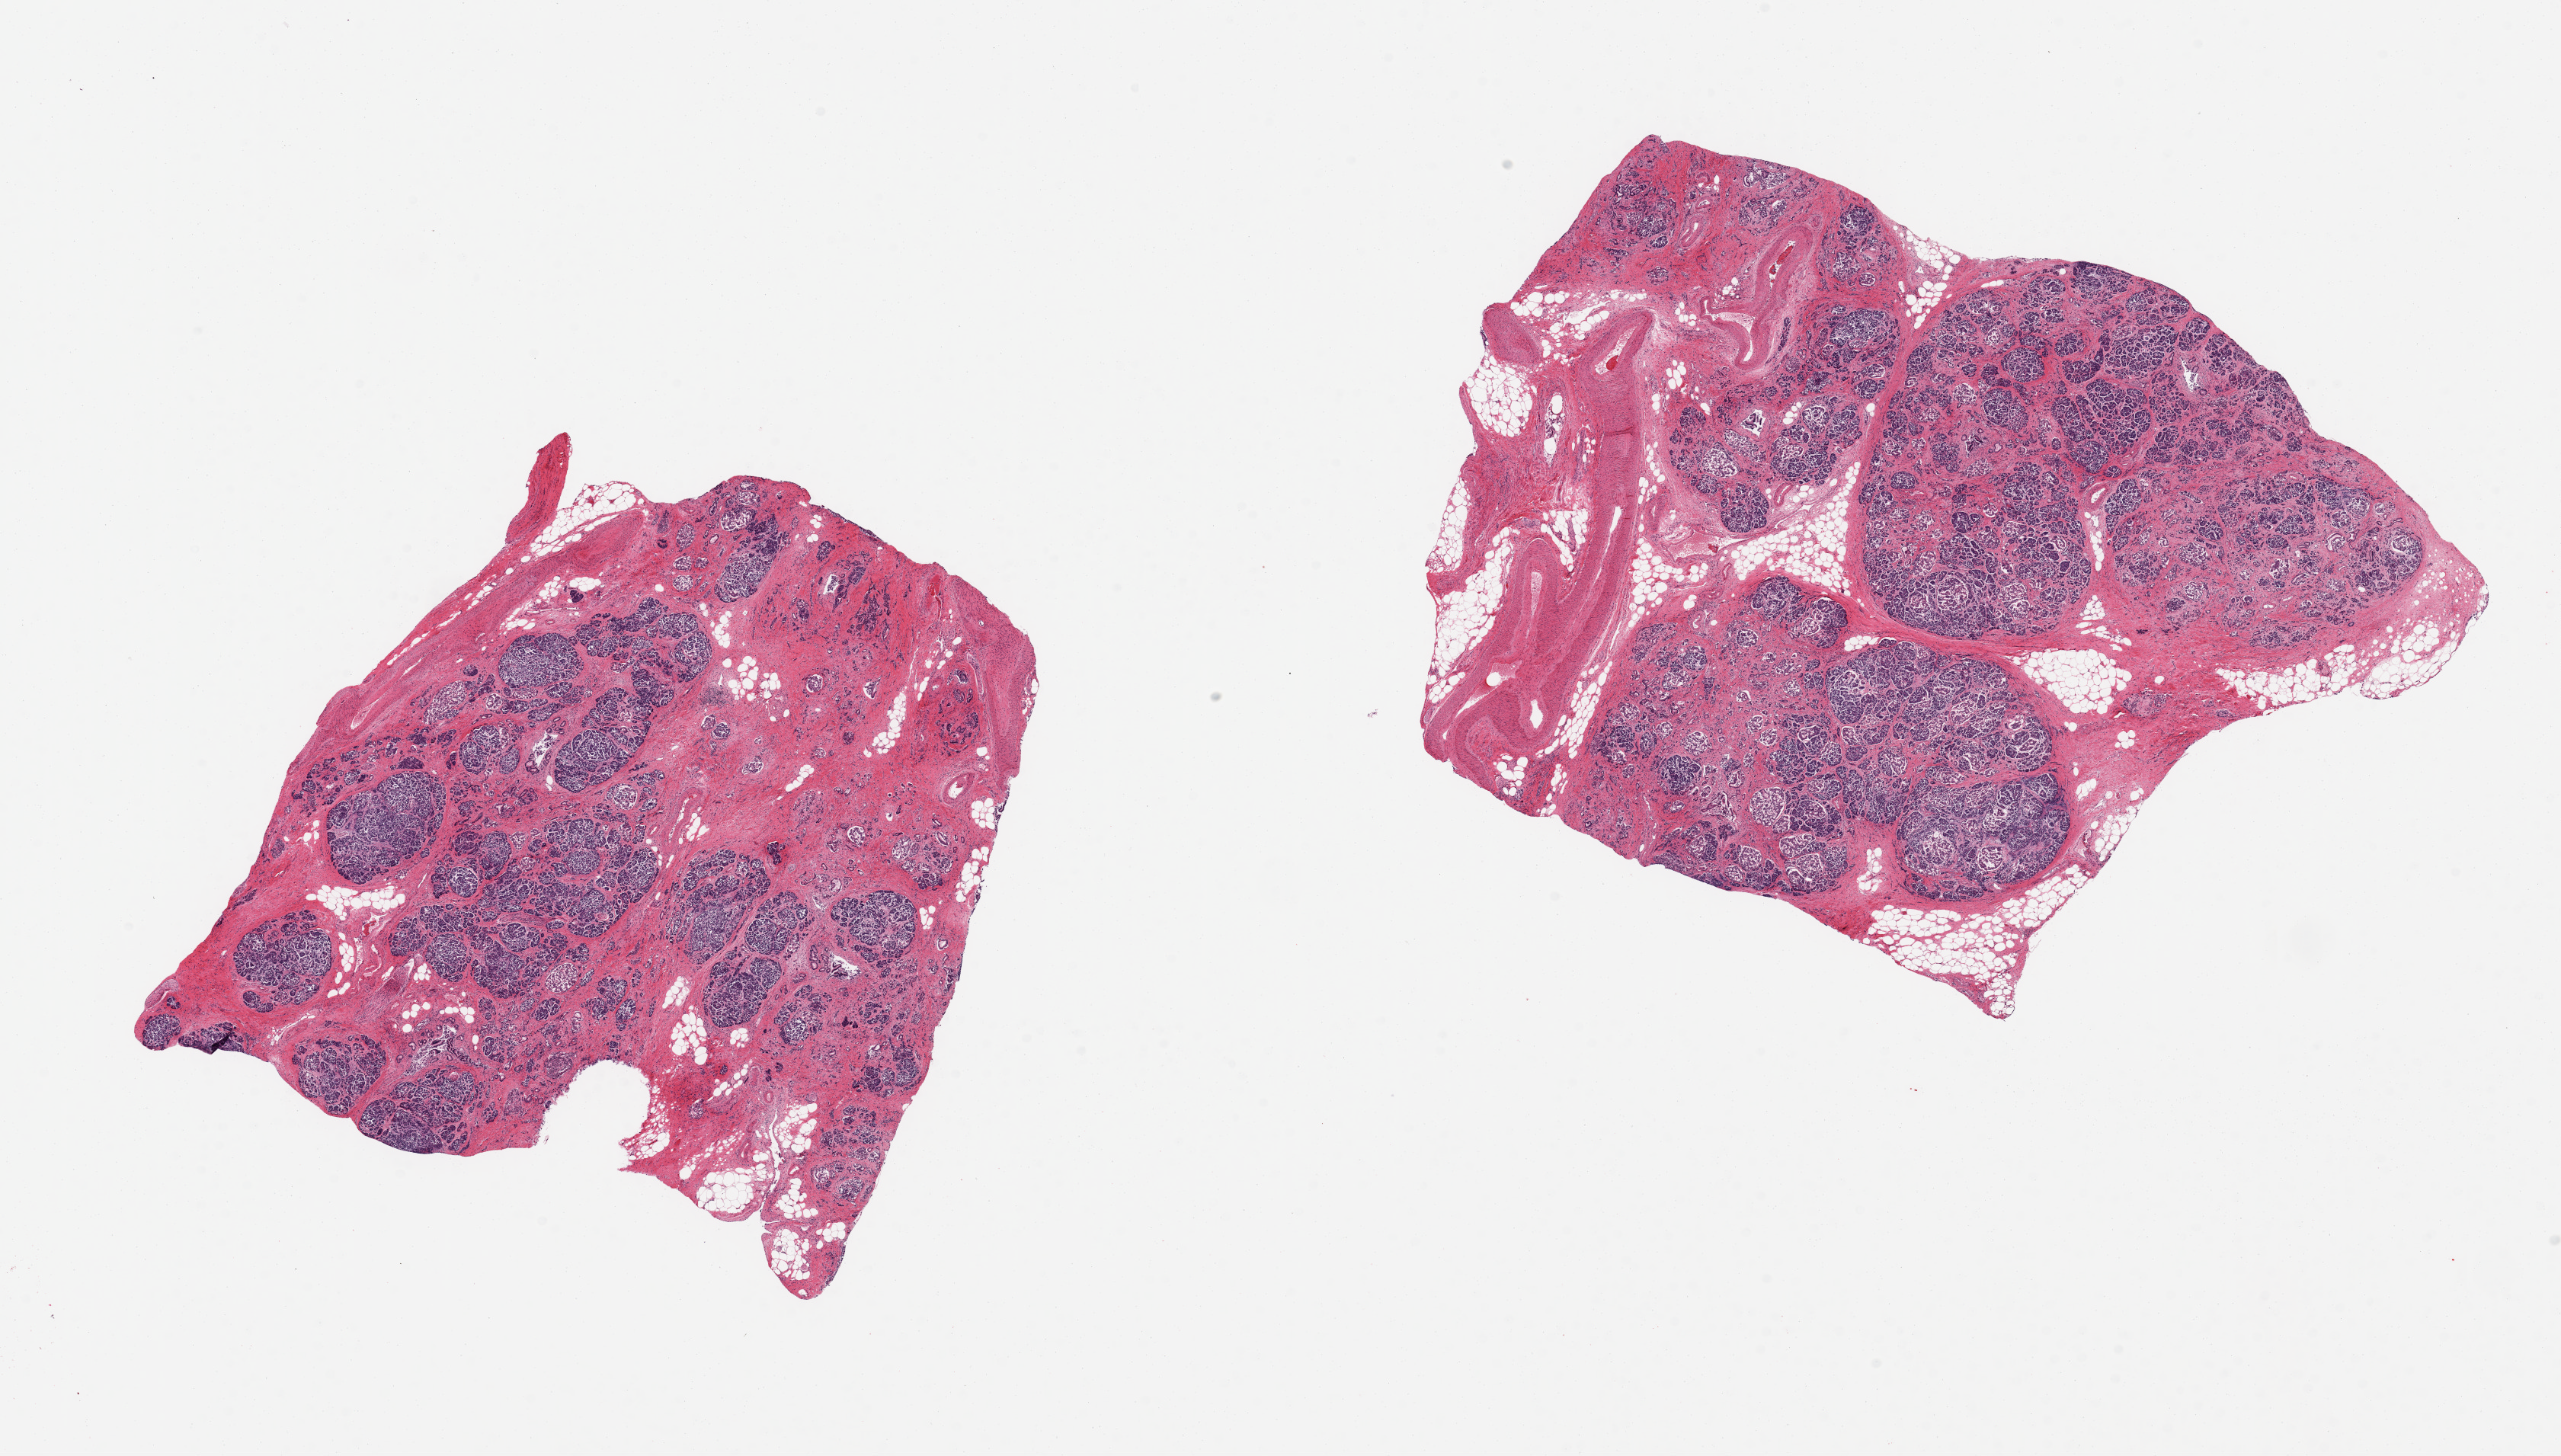
Whole-slide image, hematoxylin and eosin (H&E) stain, brightfield — low-resolution overview of the scanned area, about 26.6 x 15.1 mm (slide scanned at 20x), PAXgene-fixed paraffin-embedded (PFPE) section, target tissue: pancreas, donor tissue sample. Donor sex: male.
Review note (as recorded): 2 pieces, moderately advanced saponification; diffuse fibrosing remote pancreatitis. Few Islets dimly seen, badly autolyzed.